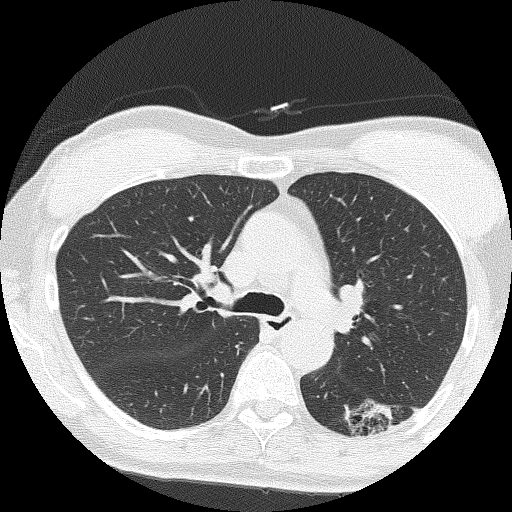
Axial slice from a low-dose chest CT screening exam, second screening round (one year after baseline), lung window (W 1500 / L -600 HU), lung (sharp) reconstruction kernel (FC51), slice 56 of 159 in the series. Female participant, aged 64 years at enrolment. Former smoker at enrolment.
- Lesion marked by an expert reader, bounding box <354,389,418,440> (left, top, right, bottom; pixels).
- The screening reader recorded 3 non-calcified nodules or masses ≥4 mm on this exam; which of them this box marks is not recorded.
- Official screen result: positive, other.
- Later outcome: lung cancer diagnosed 576 days after this screen — adenocarcinoma, NOS, left lower lobe, moderately differentiated (G2), stage IA (AJCC 6th edition), 17 mm at pathology.